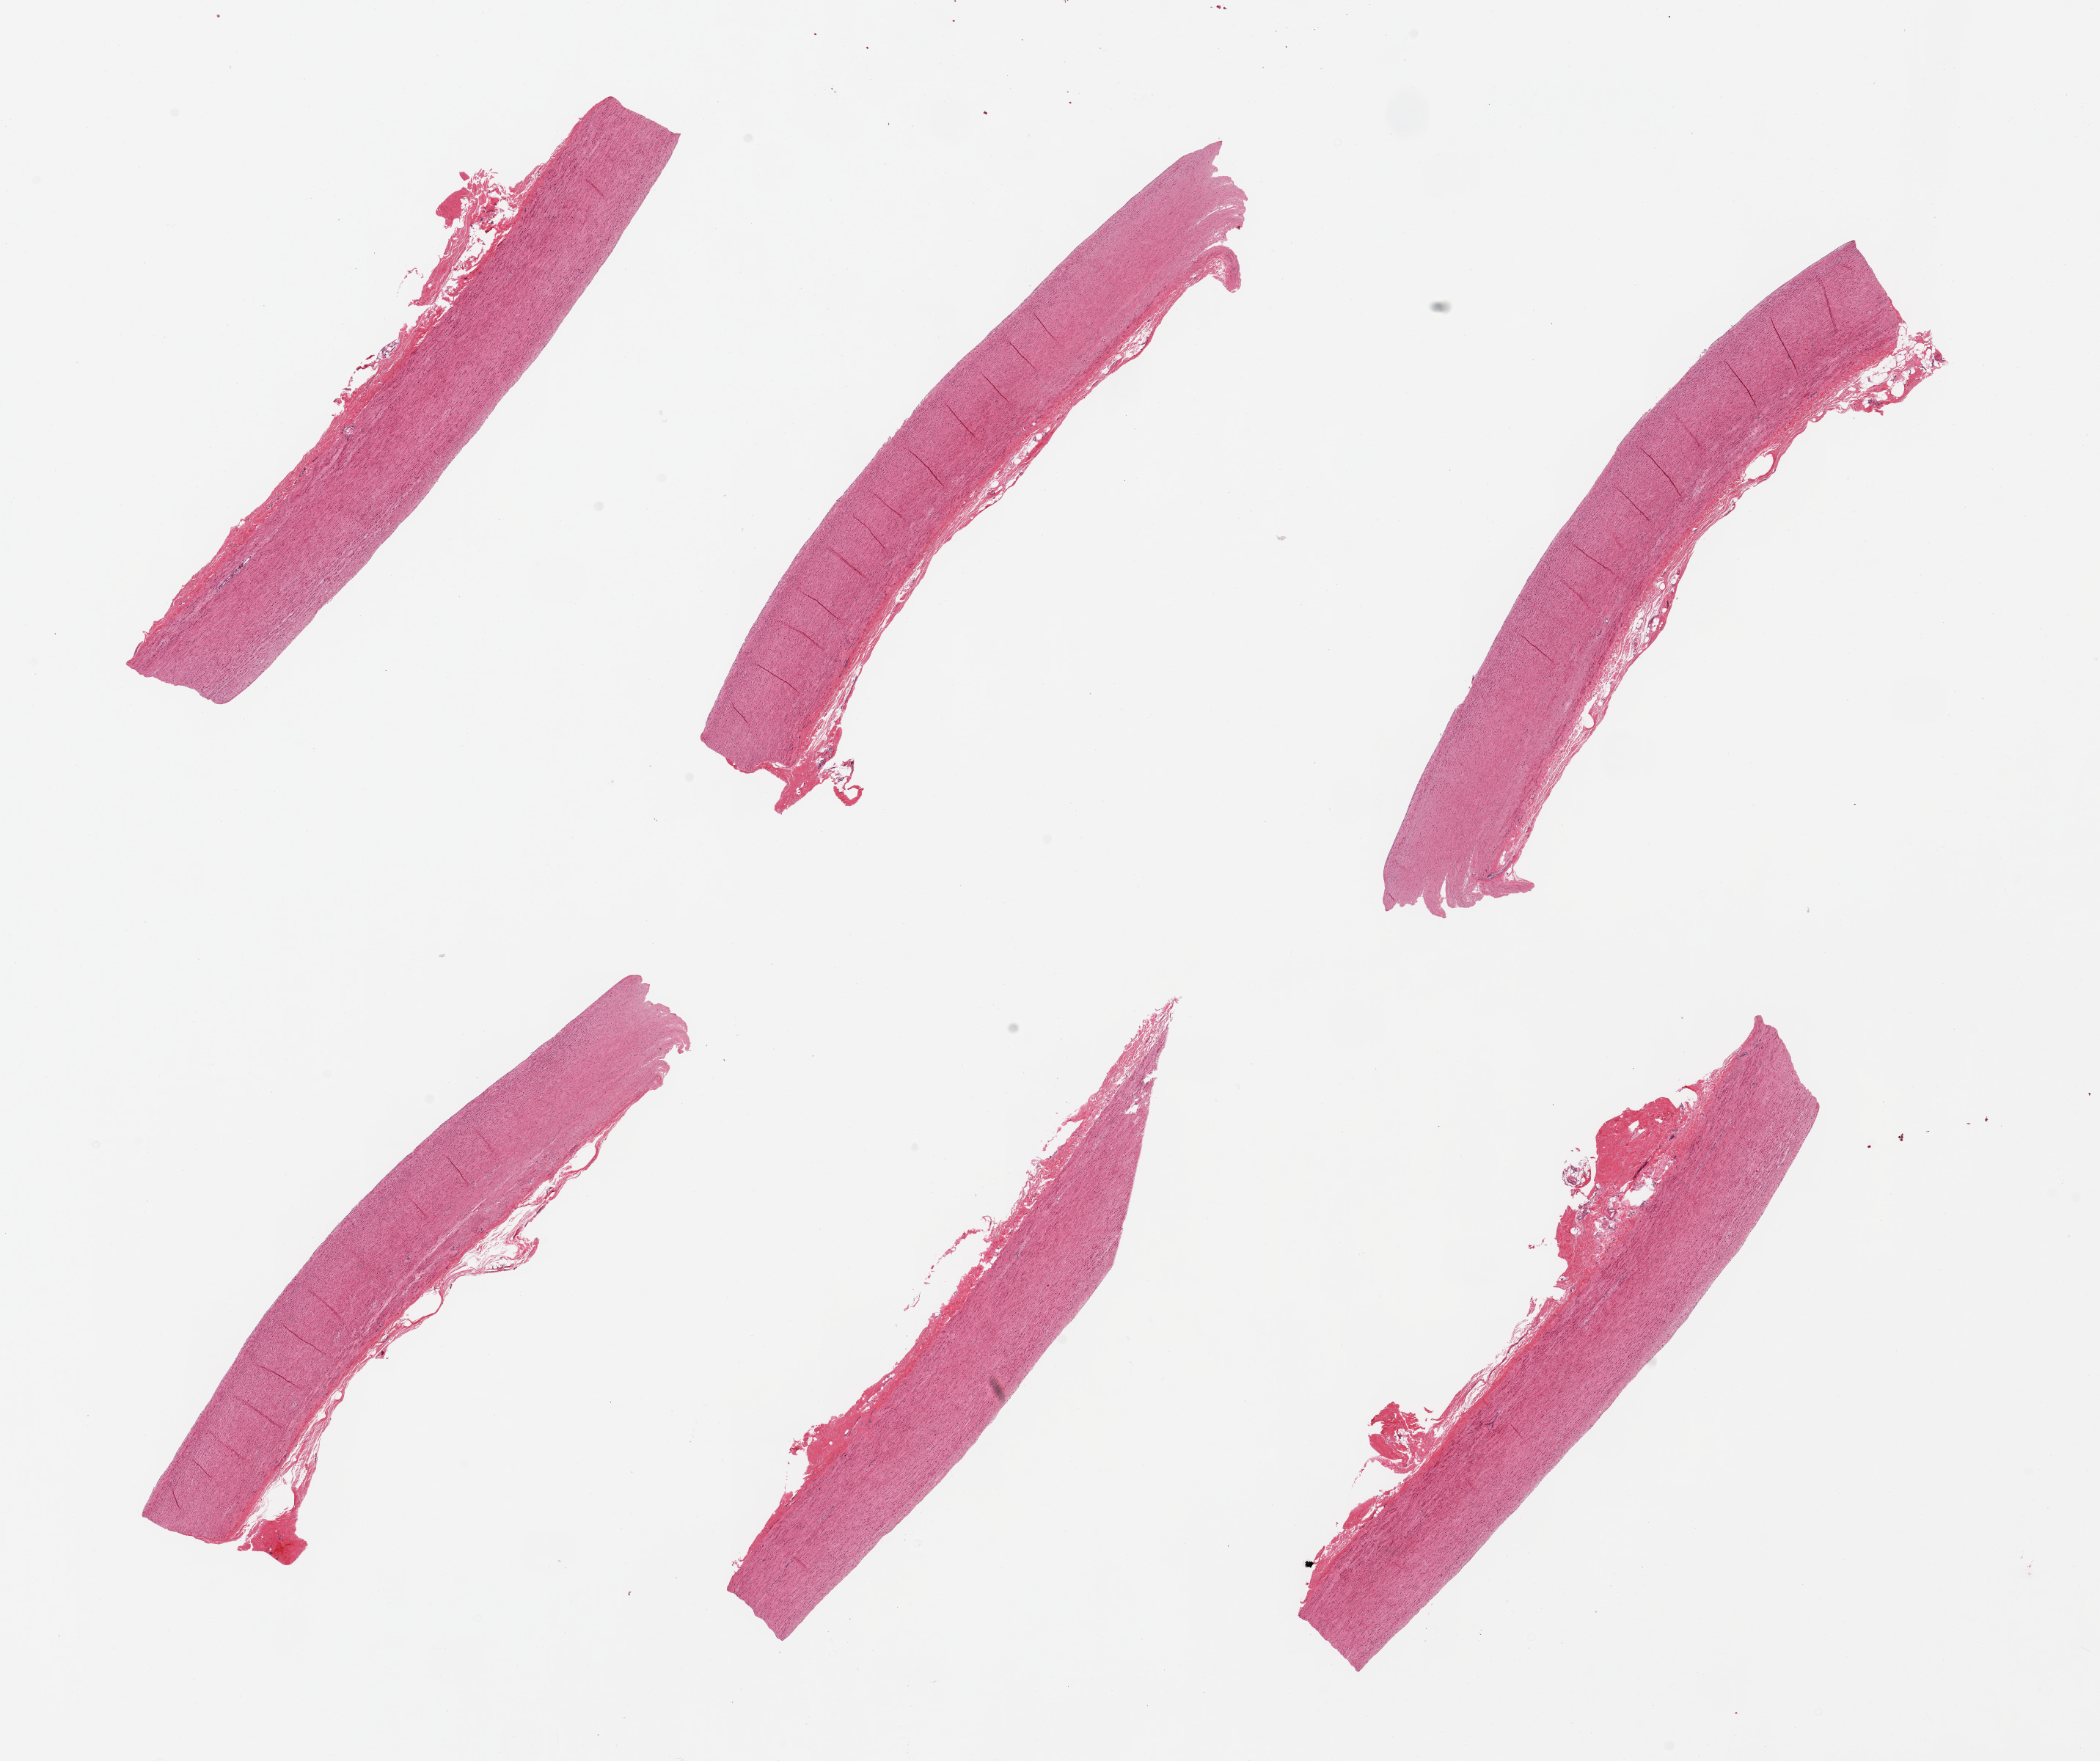
Digitized hematoxylin and eosin (H&E)-stained section — low-resolution overview of the scanned area, about 22.6 x 19.0 mm. PAXgene-fixed, paraffin-embedded tissue. Sampled site (target tissue): aorta. Tissue donor sample. Male donor.
Review note (as recorded): 6 pieces; no lesions; well trimmed.